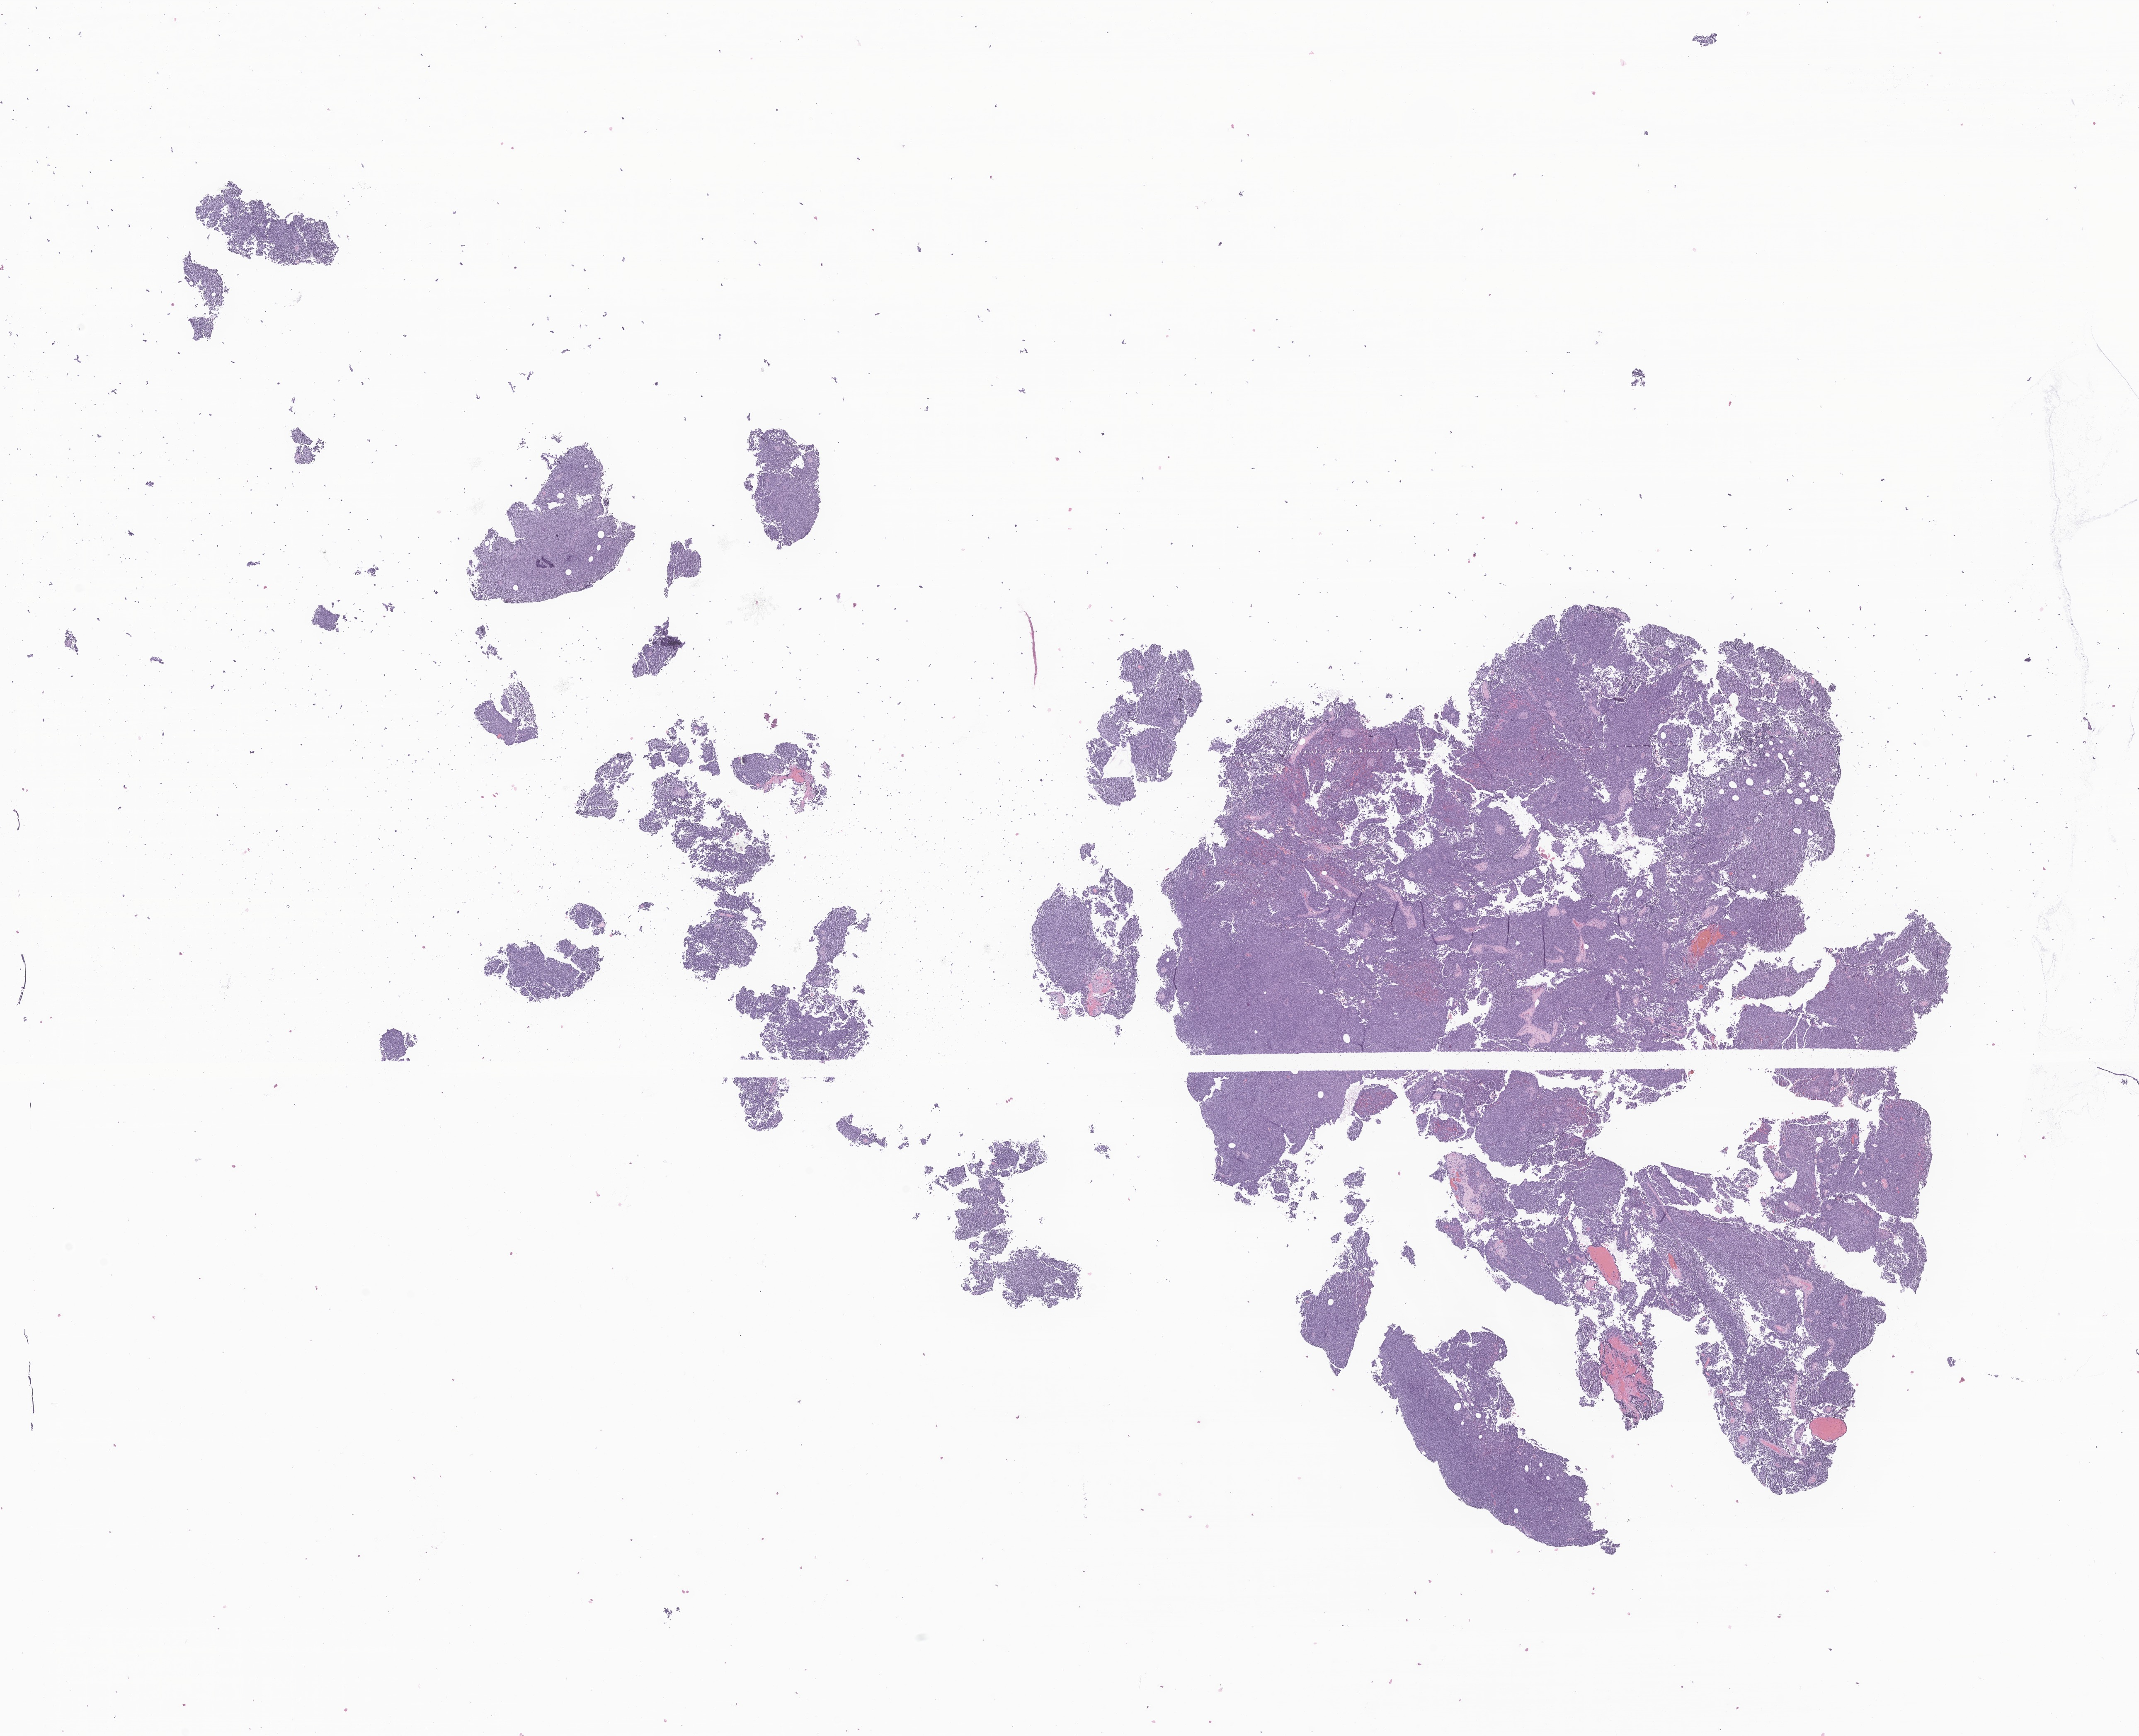
H&E whole-slide image of tumor tissue from the anterior mediastinum — low-resolution overview of the scanned area, about 21.8 x 17.7 mm. Formalin-fixed paraffin-embedded section. Patient male; age 164 days.
Recorded diagnosis: Rhabdomyosarcoma, NOS.